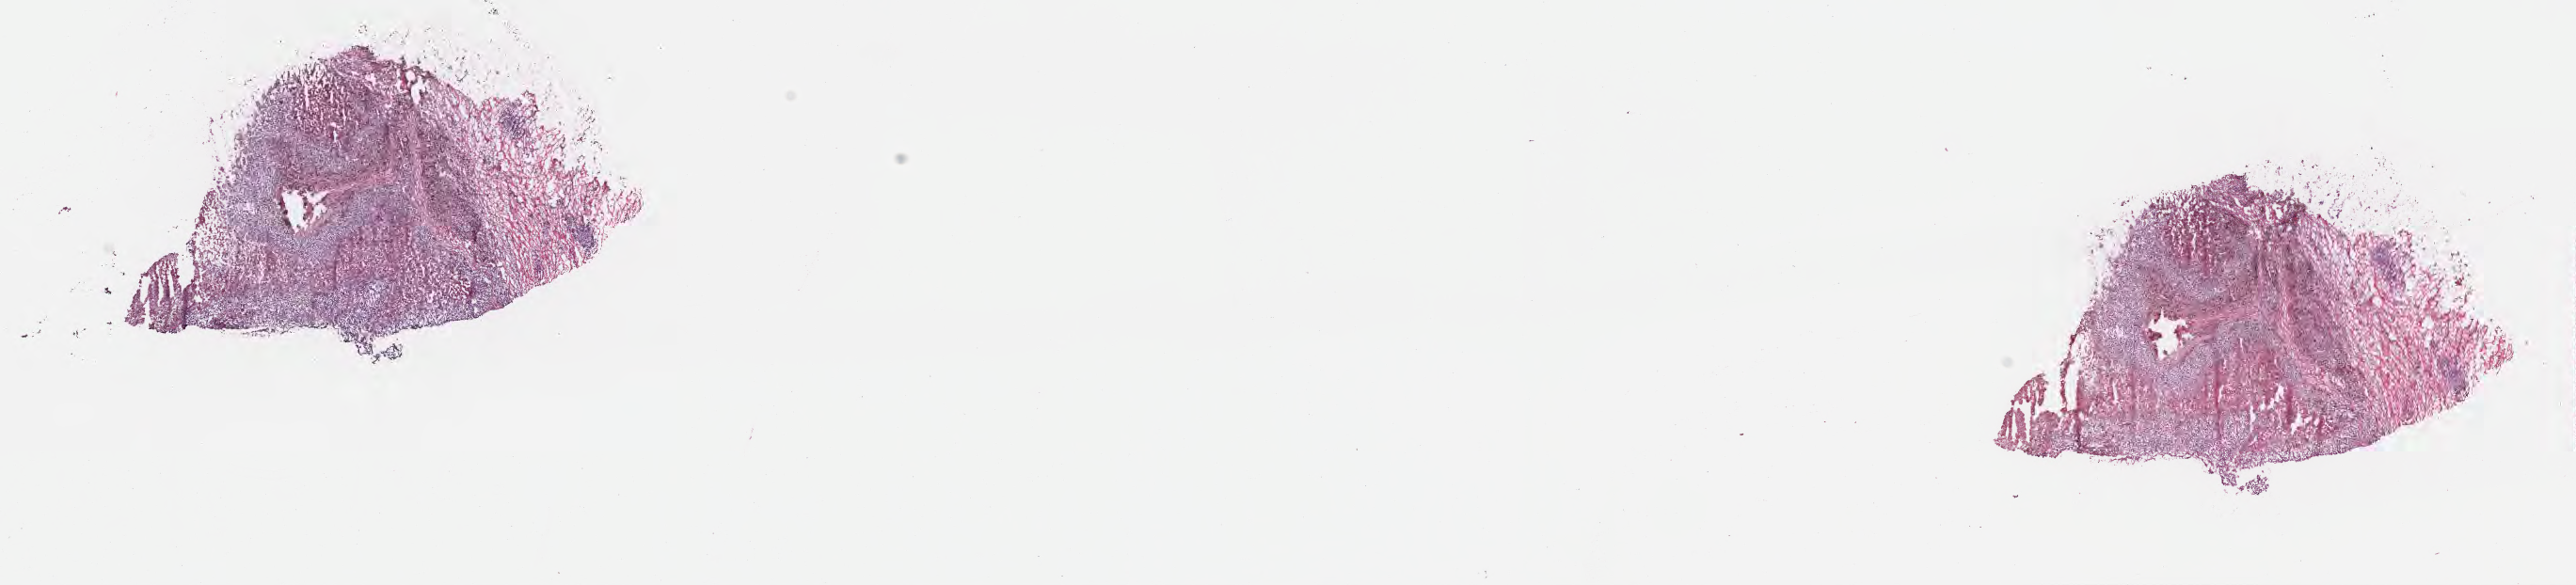
Digitized H&E-stained section — a low-resolution overview of the entire scanned area, about 22.1 x 5.0 mm; cryosection; specimen: metastatic tumor tissue, resected from lymph nodes of inguinal region or leg. Female patient; age at initial diagnosis 45 years. Pathologist review of this section (percent, as recorded): tumor cells 35%, tumor nuclei 65%, stromal cells 0%, necrosis 35%, normal cells 30%. Inflammatory infiltration, as recorded: lymphocyte infiltration 0%, monocyte infiltration 0%, neutrophil infiltration 0%.
Patient diagnosis (primary): Malignant melanoma, NOS. Section: bottom of the tissue portion.